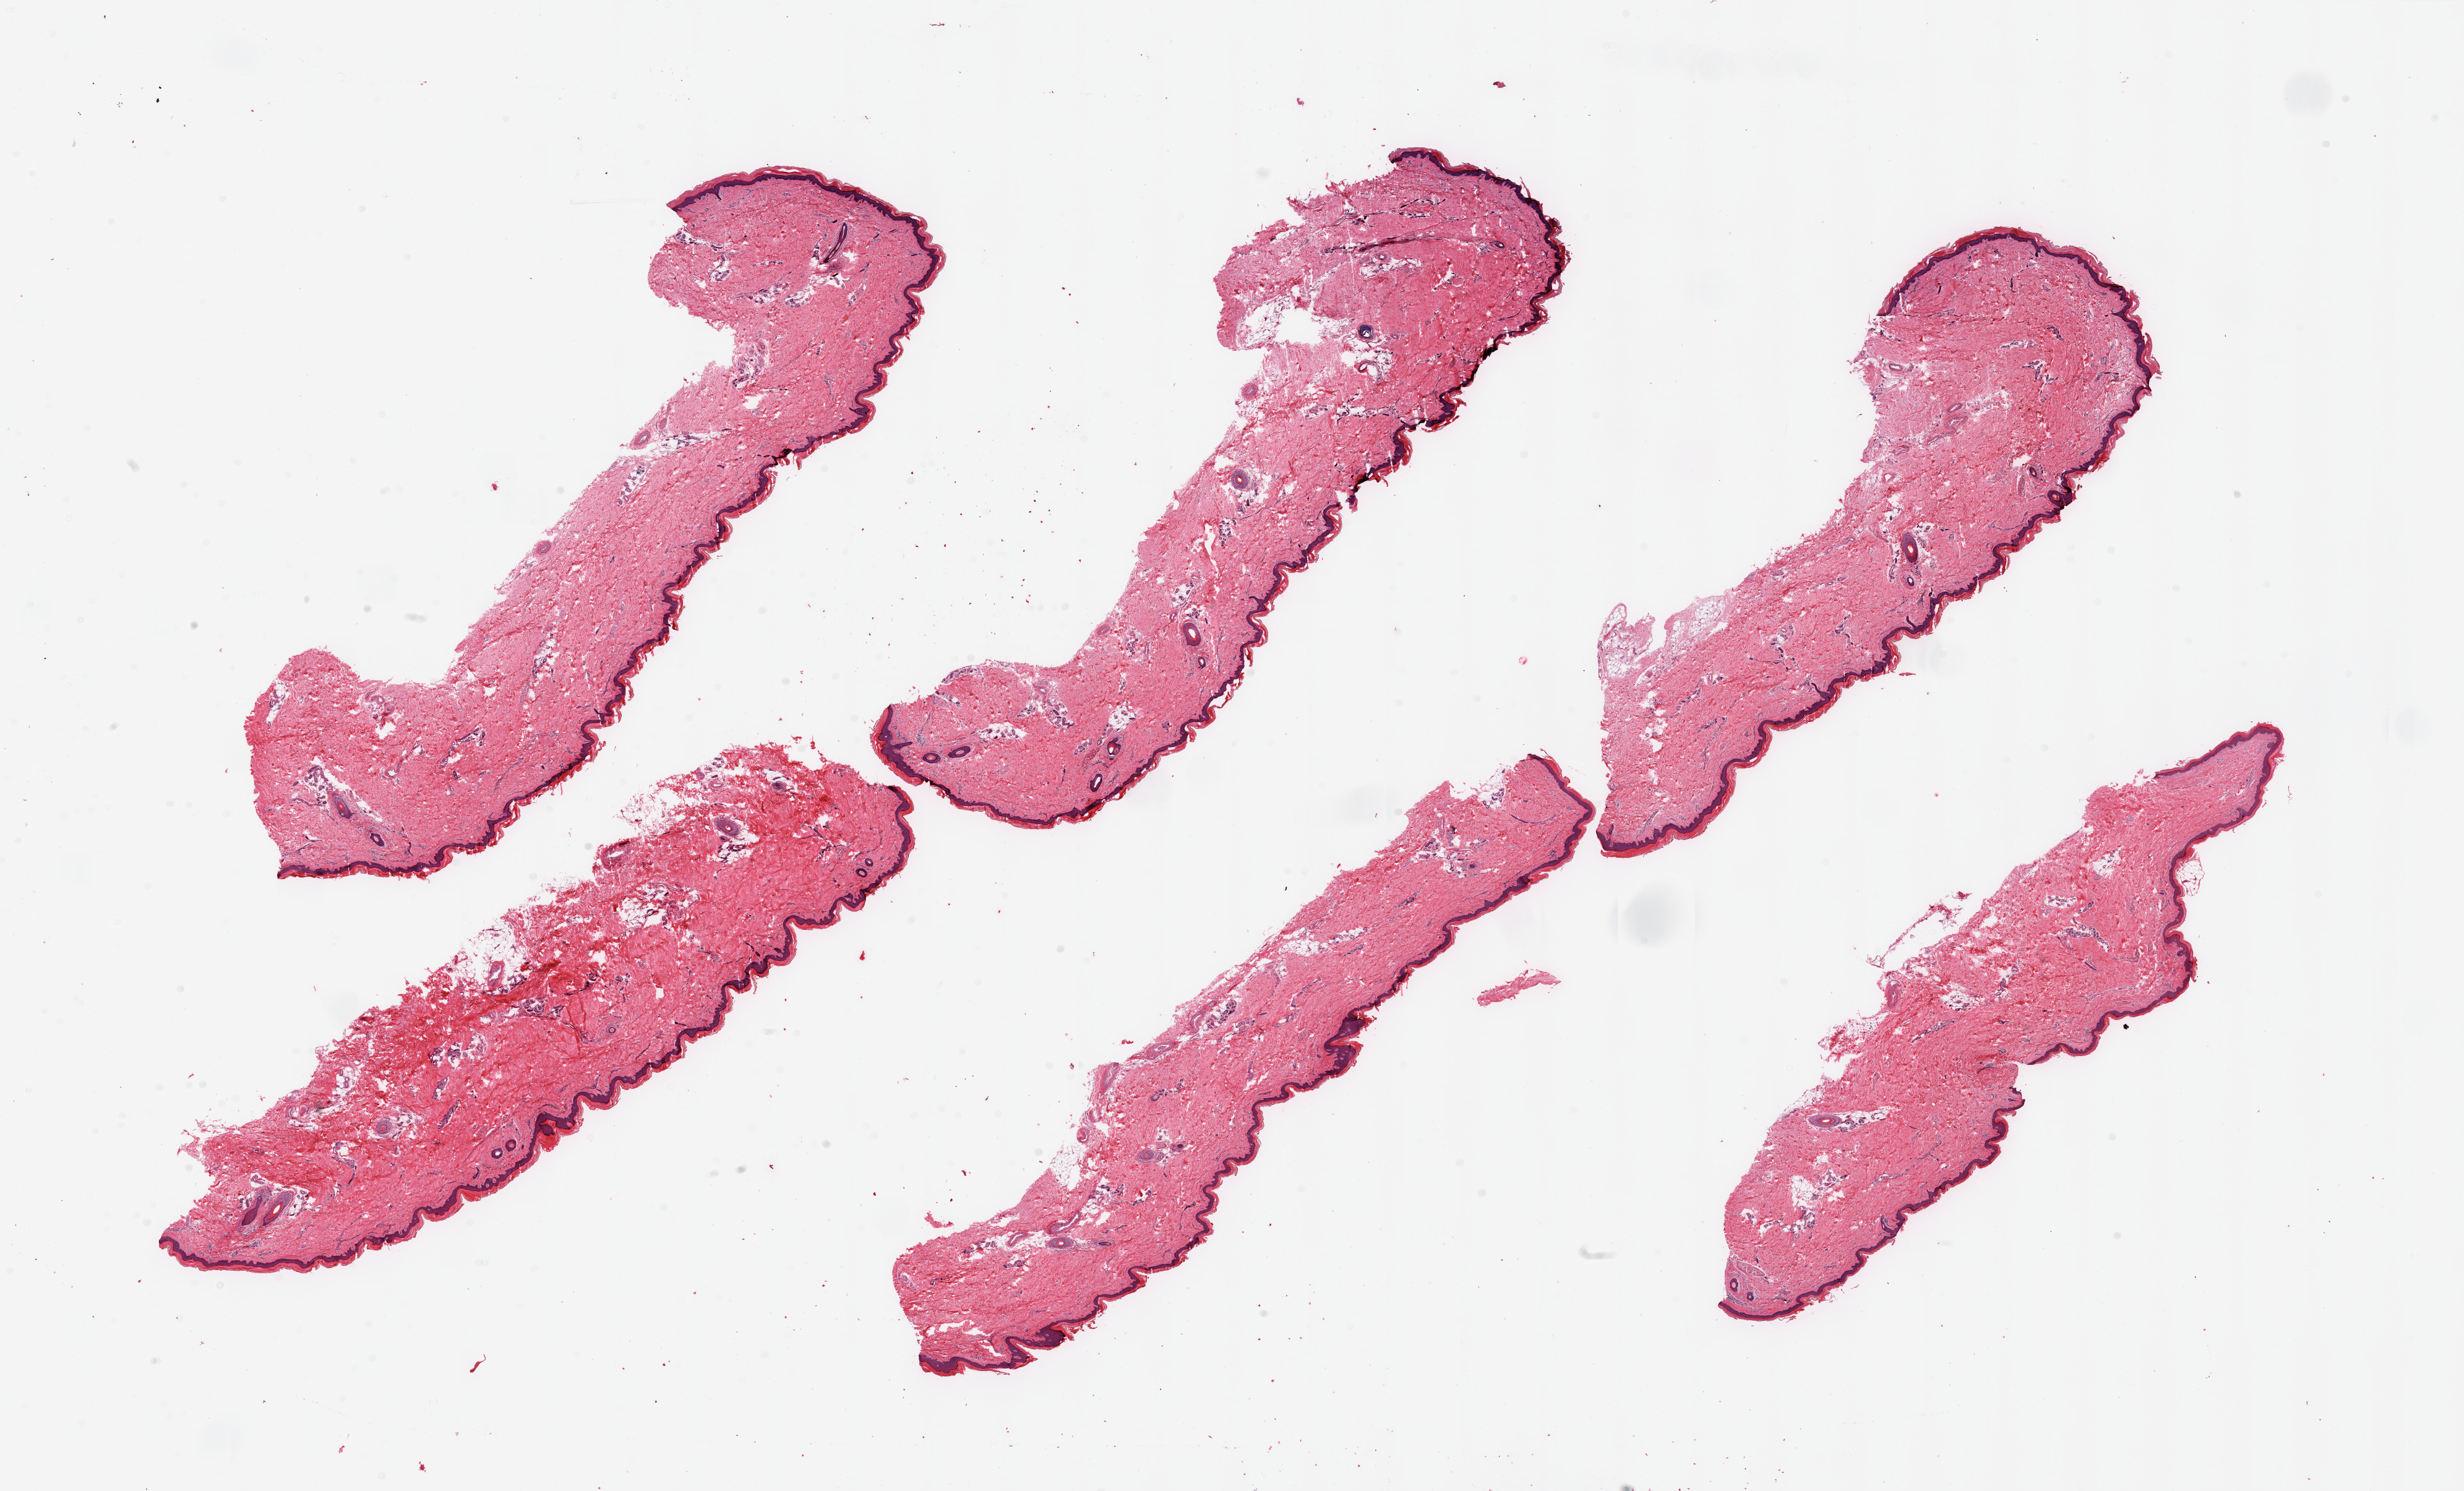
Whole-slide image, H&E stain — shown as a low-resolution overview of the whole scanned area (about 31.5 x 19.1 mm, slide scanned at 20x). PAXgene-fixed paraffin-embedded (PFPE) section. Section of skin of lower leg (target tissue). Donor tissue sample. Donor: female.
- reviewer comment on this tissue sample: 6 pieces, no dermal fat; squamous epithelium is ~ 40-50 microns